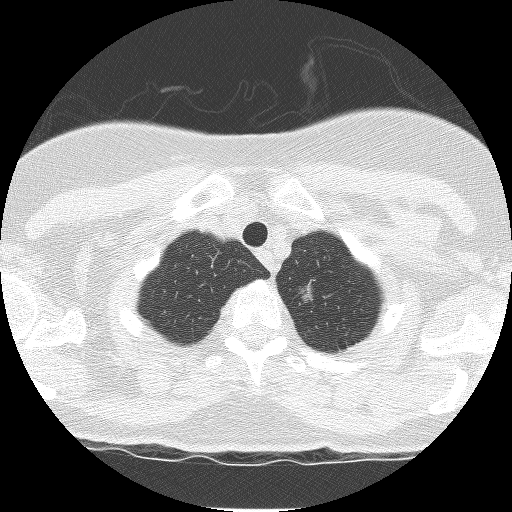
Axial slice from a low-dose chest CT screening exam, third screening round (two years after baseline), lung window (W 1500 / L -600 HU), lung (sharp) reconstruction kernel (BONE), 120 kVp. Female, age 59 years at enrolment. Former smoker at enrolment.
Expert reader's lesion annotation, box from (x=274, y=267) to (x=330, y=322) px. The screening reader recorded 3 non-calcified nodules or masses ≥4 mm on this exam (right upper lobe, left upper lobe, right upper lobe); which of them this box marks is not recorded. Official screen result: positive, other. Lung cancer was diagnosed 42 days after this screen: bronchiolo-alveolar adenocarcinoma, NOS, left upper lobe, well differentiated (G1), stage IA (AJCC 6th edition), 10 mm at pathology.